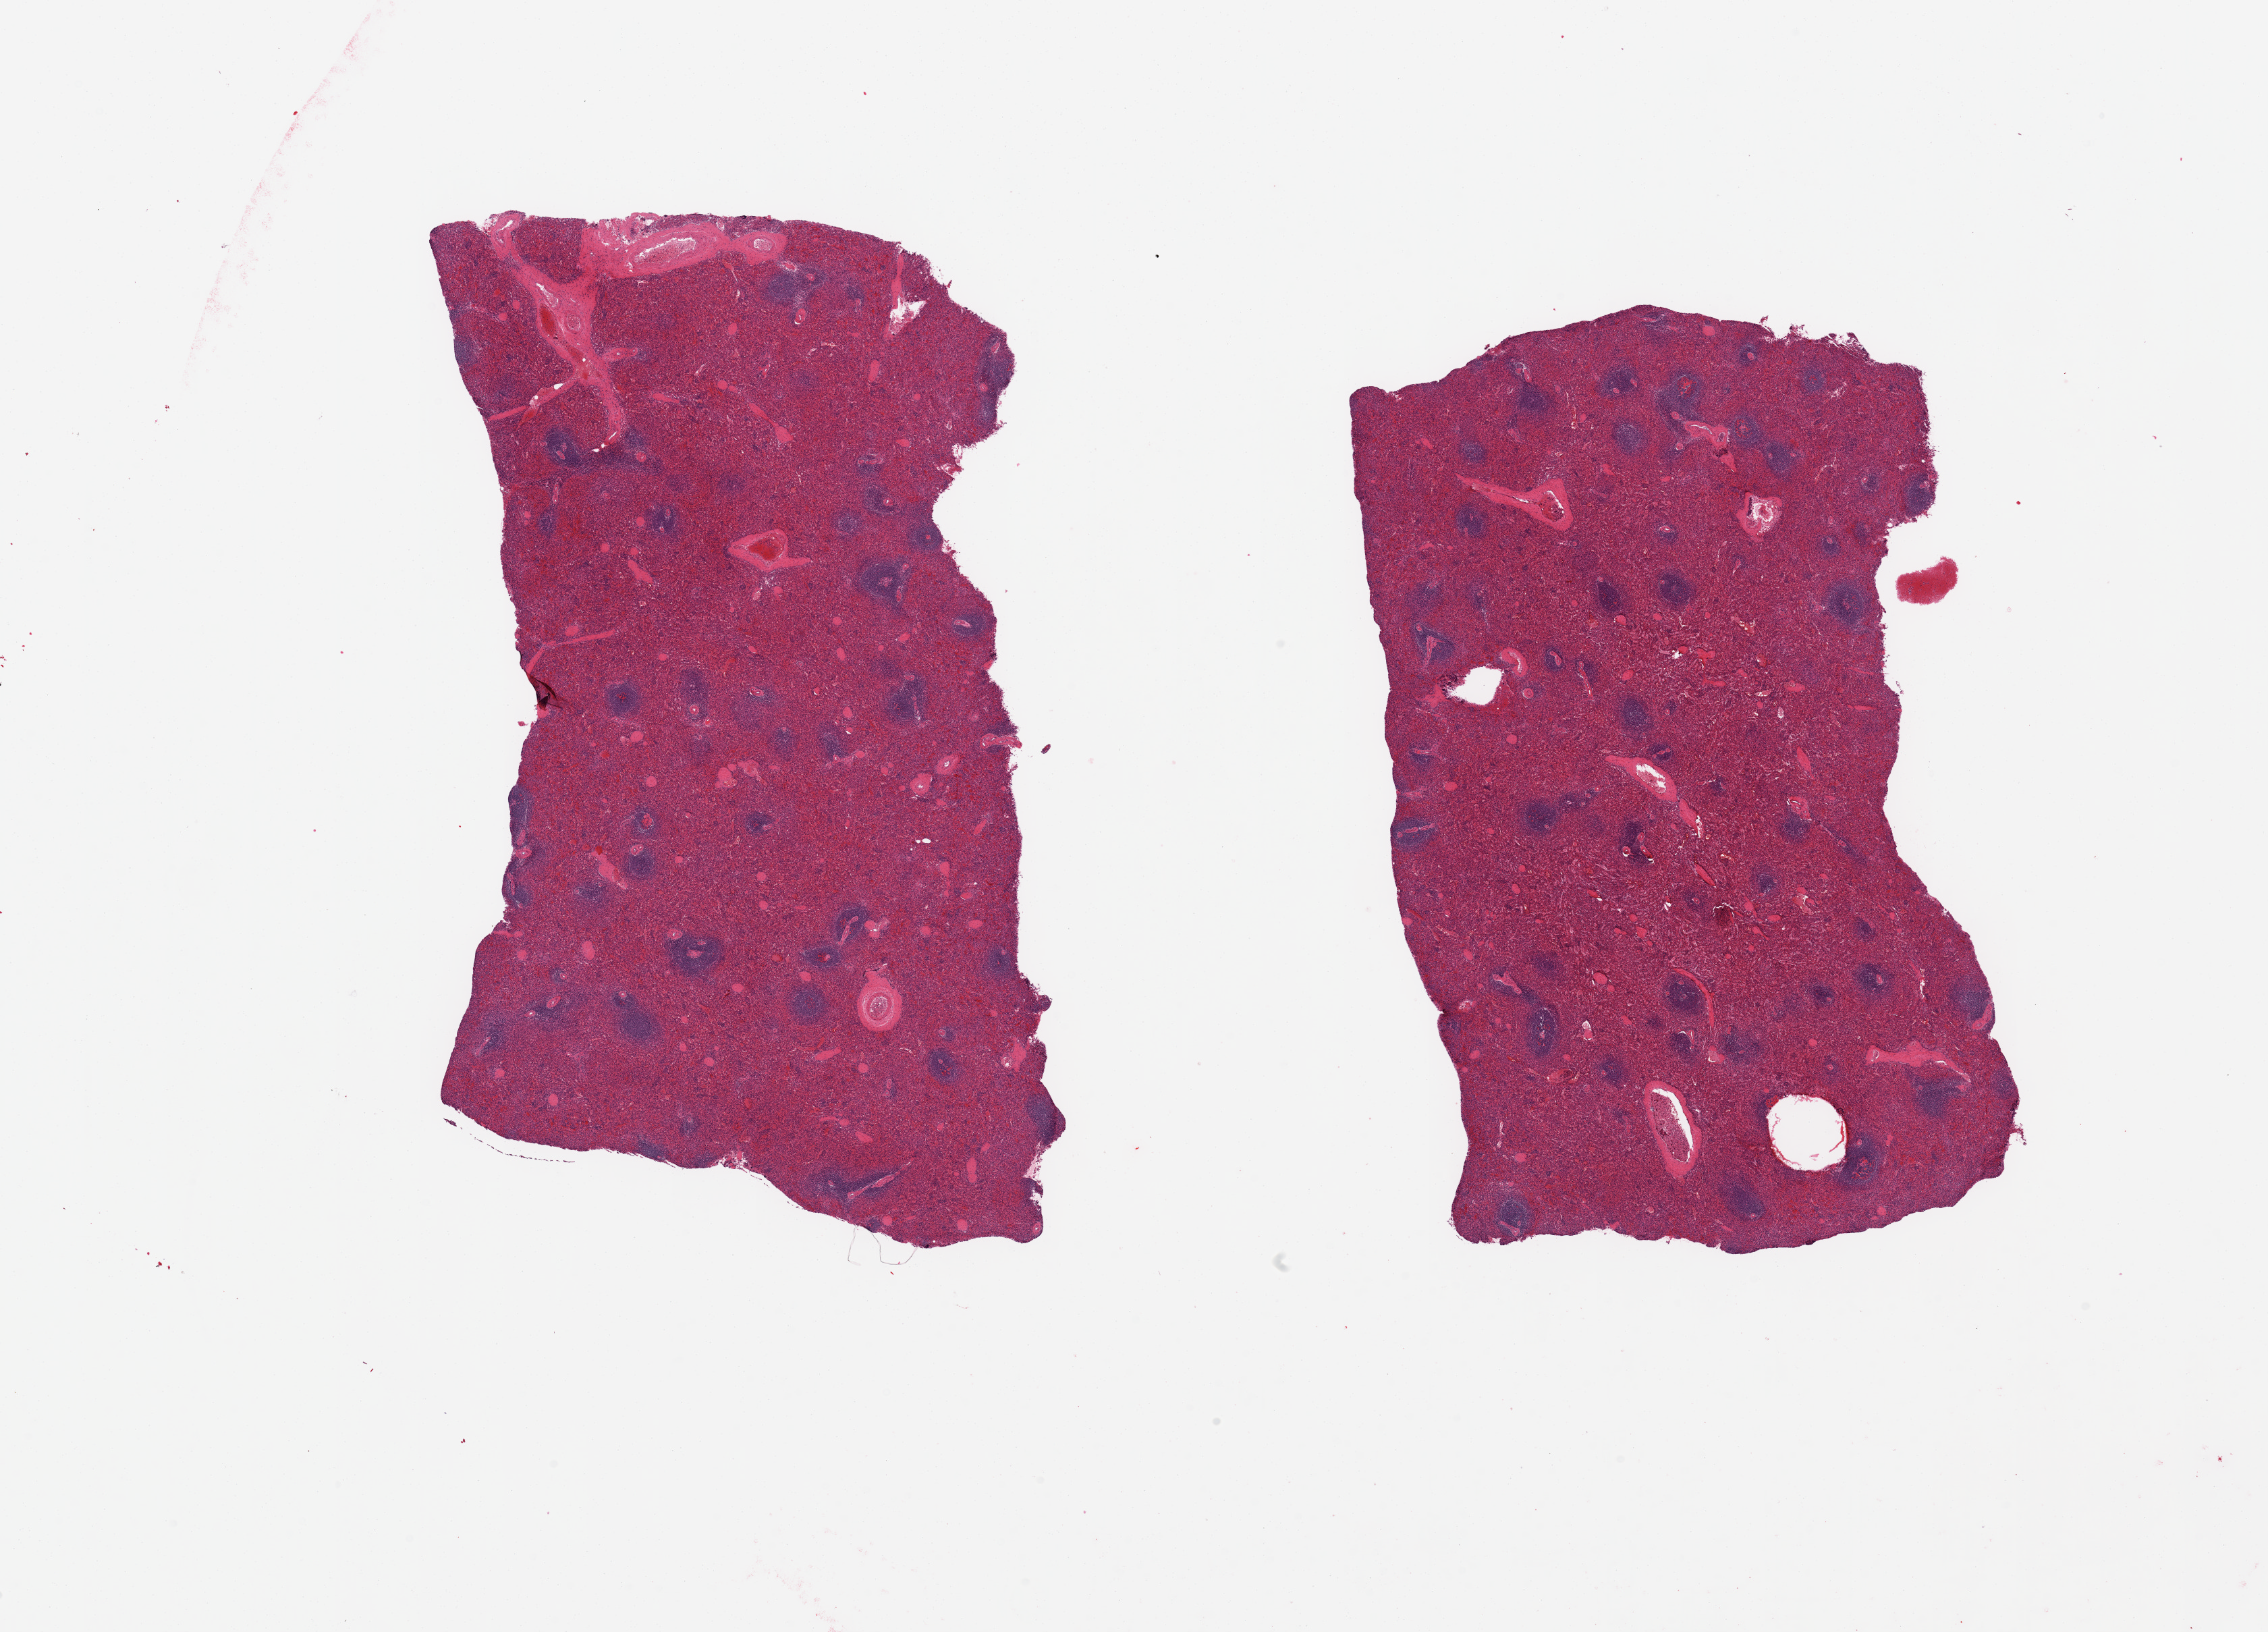
Whole-slide image, haematoxylin and eosin stain — whole scanned area (about 26.6 x 19.1 mm, acquisition: 20x scan) shown as a low-resolution overview, PAXgene-fixed, paraffin-embedded tissue, sampled site (target tissue): spleen, tissue donor sample. Donor sex: female.
Review note (as recorded): 2 pieces.